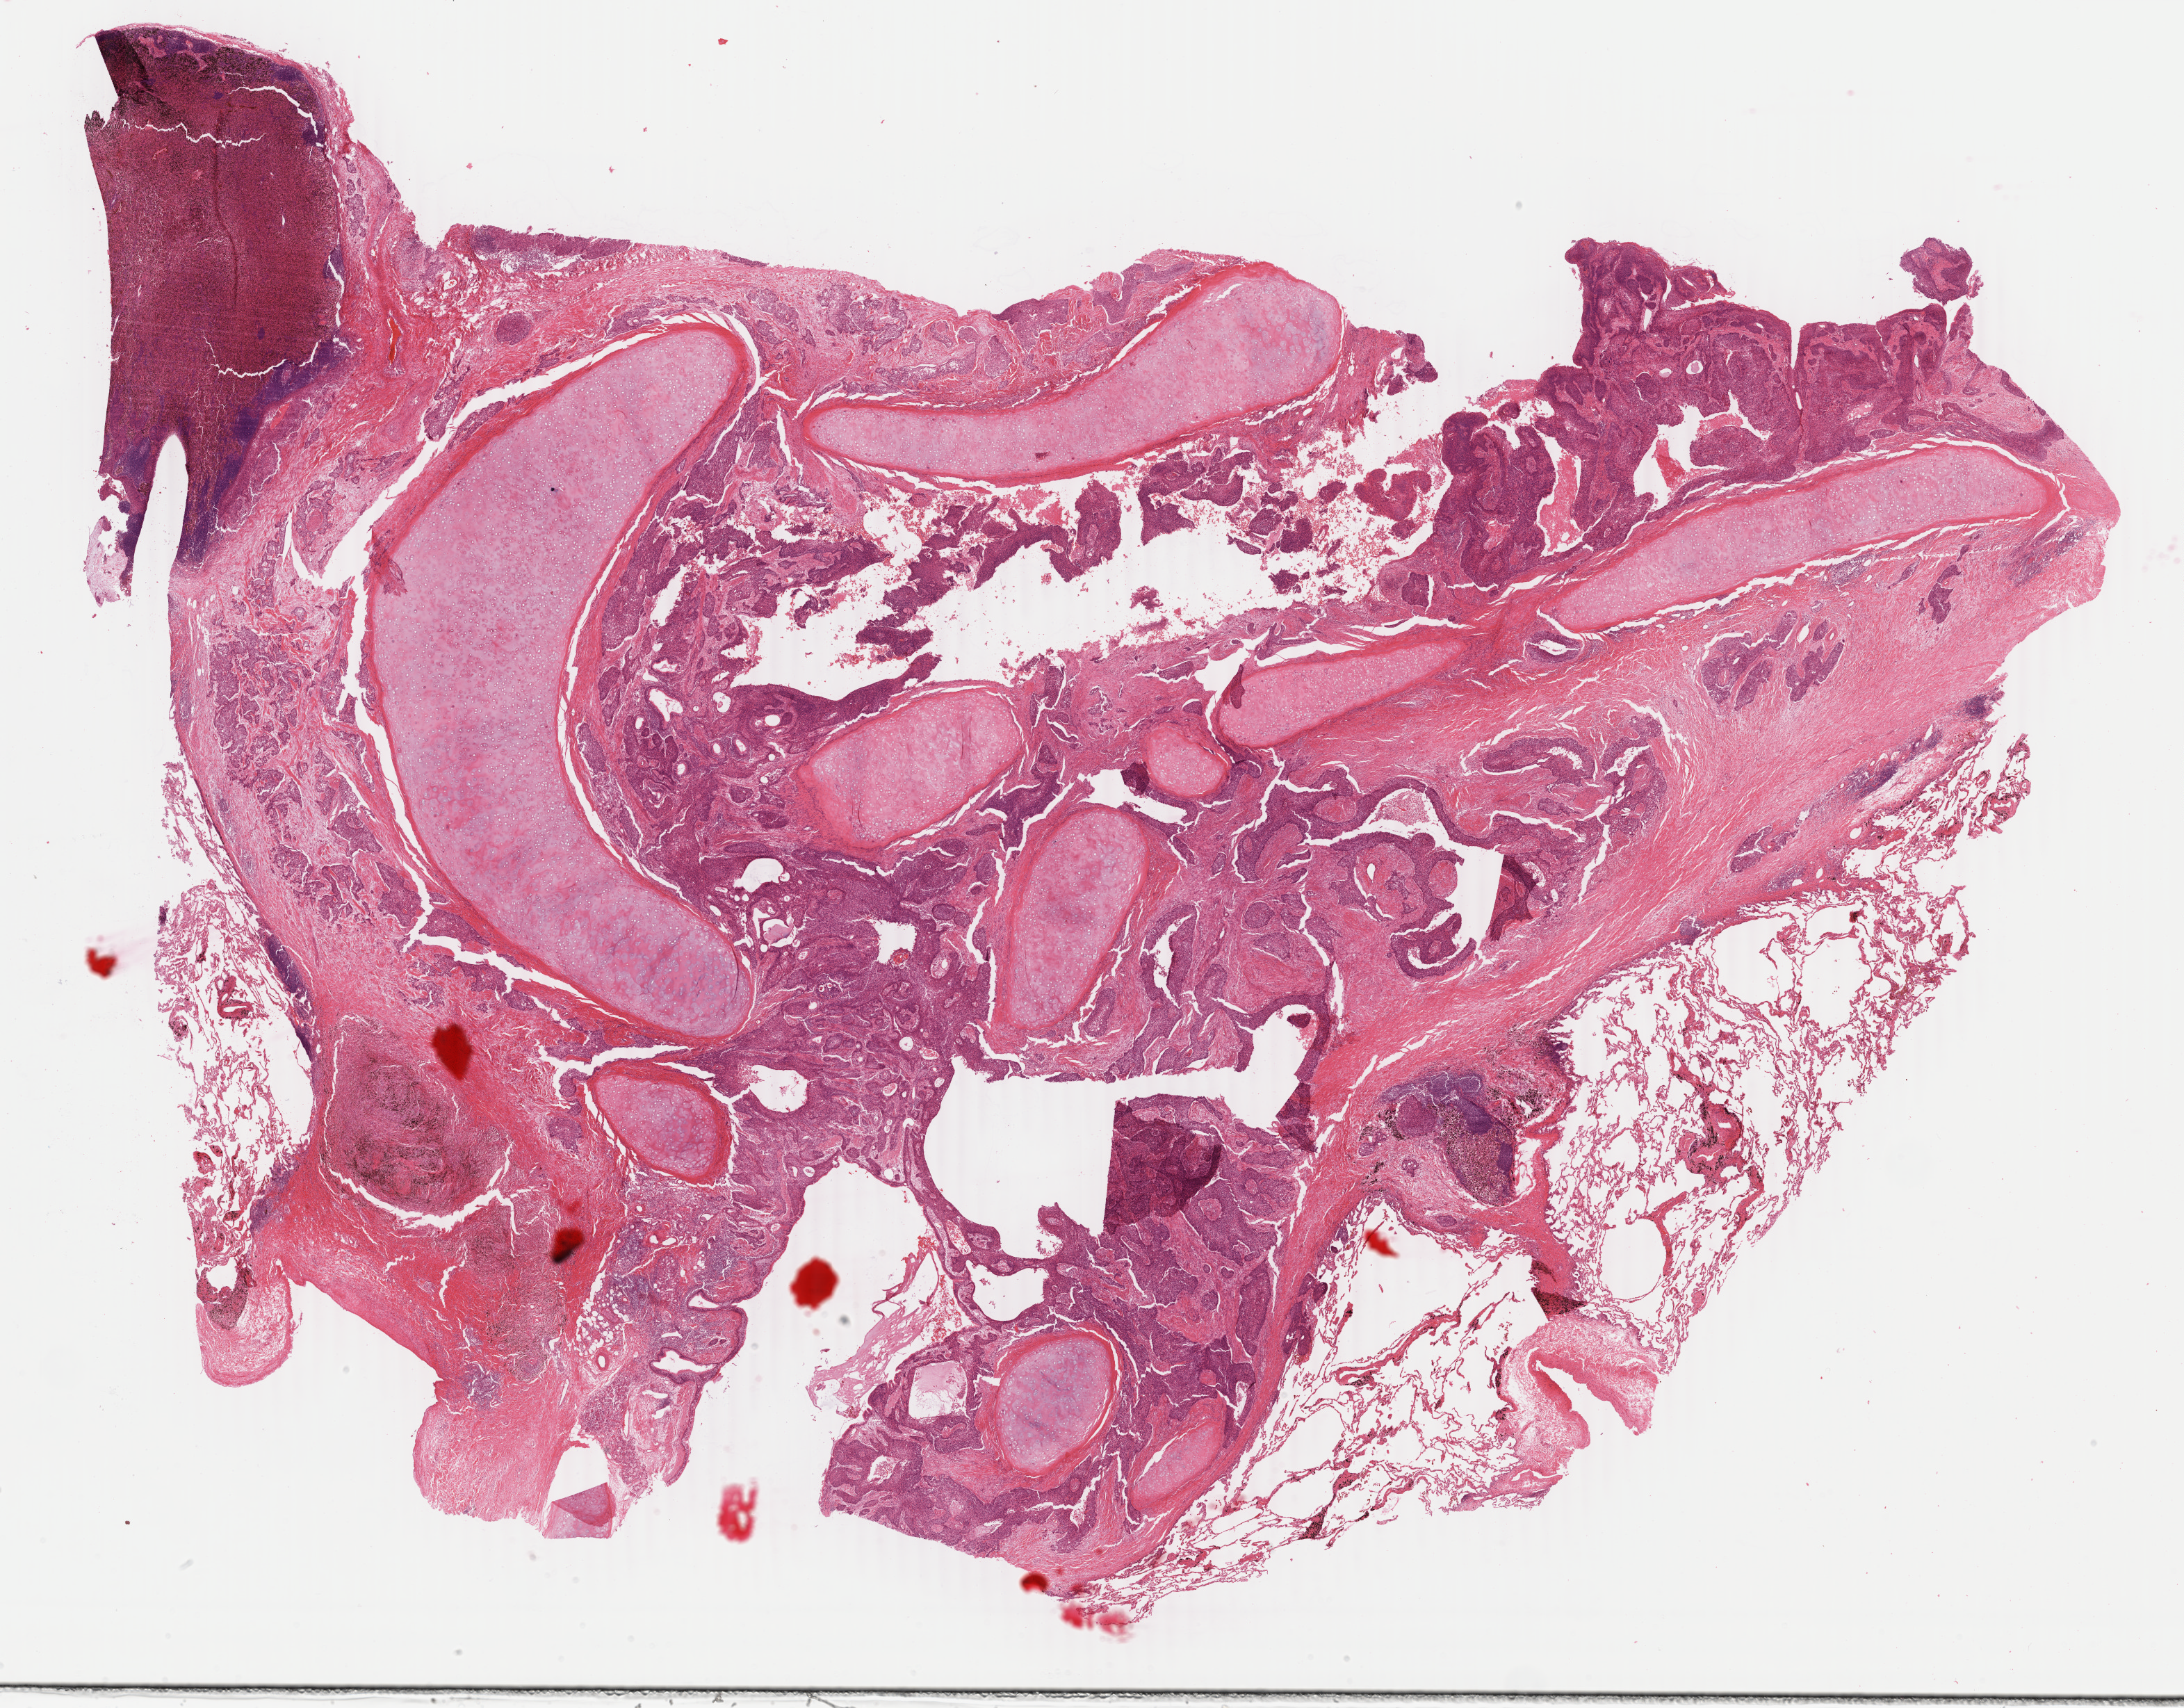
Digitized Hematoxylin and eosin (H&E) stained tissue section (whole slide) — a low-resolution overview of the entire scanned area, about 25.0 x 19.5 mm (from a 40x scan), formalin-fixed paraffin-embedded (FFPE) diagnostic section, lung, primary tumour sample. Male, age 58 years at initial diagnosis.
Pathologic diagnosis: Squamous cell carcinoma, NOS (upper lobe, lung).